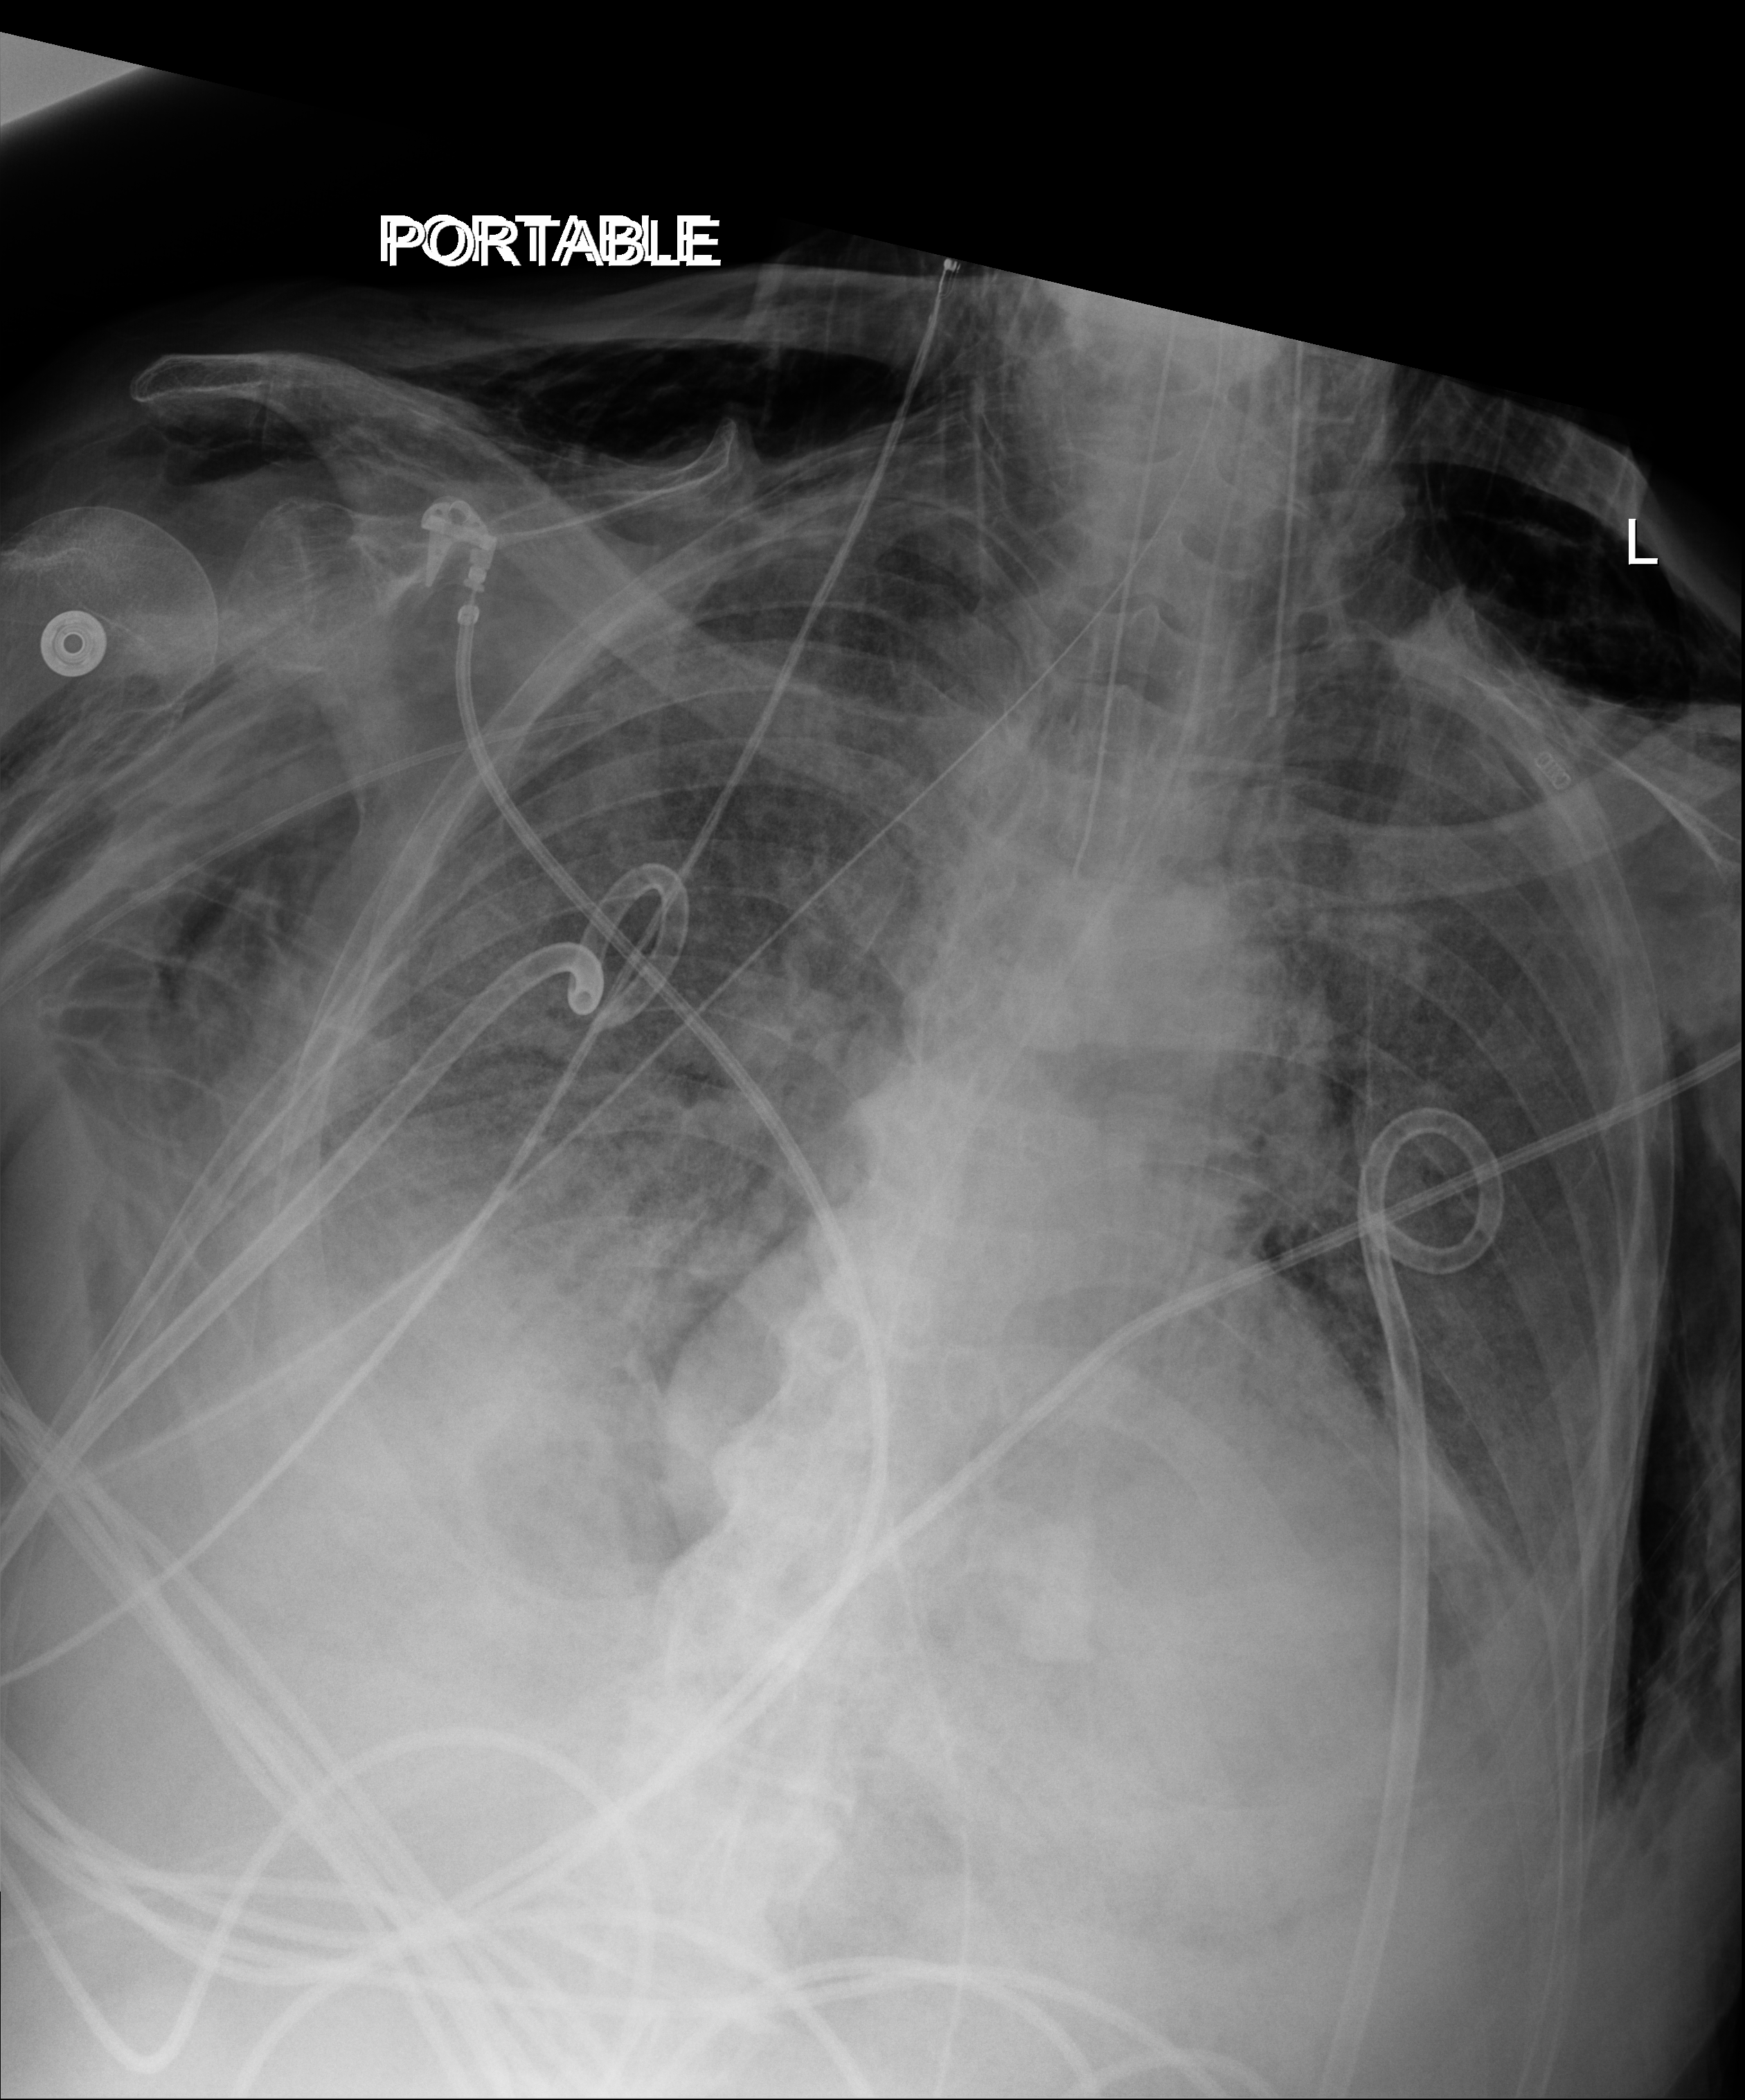
Chest X-ray (portable). Male patient hospitalised with COVID-19, age 75–90 years.
Hospital-stay facts (about this admission, not read from this image; timing relative to this image not recorded): diabetes (admission record): no.